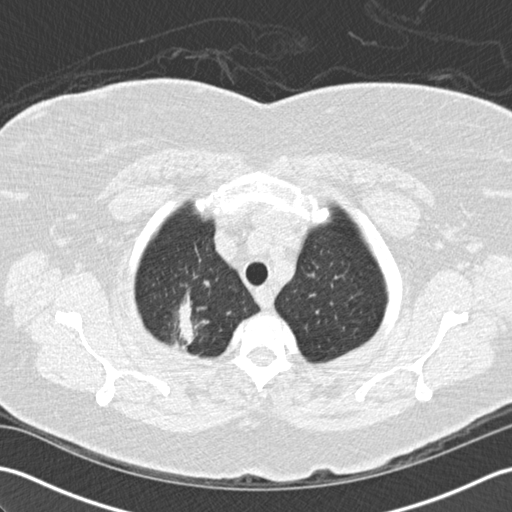
Chest CT (low-dose screening protocol), one axial image. First (baseline) screen. Lung window (W 1500 / L -600 HU). 2 mm slice thickness. Slice 21 of 156 in the series. 512 × 512 image matrix. Female, age 72 years at enrolment. Former smoker at enrolment.
Expert-annotated lung lesion, bounding box [x1, y1, x2, y2] px = [136, 276, 226, 366]. The screening reader recorded 2 non-calcified nodules or masses ≥4 mm on this exam; which of them this box marks is not recorded. Lung cancer was diagnosed 494 days after this screen (after the second annual screen): bronchiolo-alveolar adenocarcinoma, NOS, right upper lobe, stage IIIB (AJCC 6th edition), 45 mm at pathology.